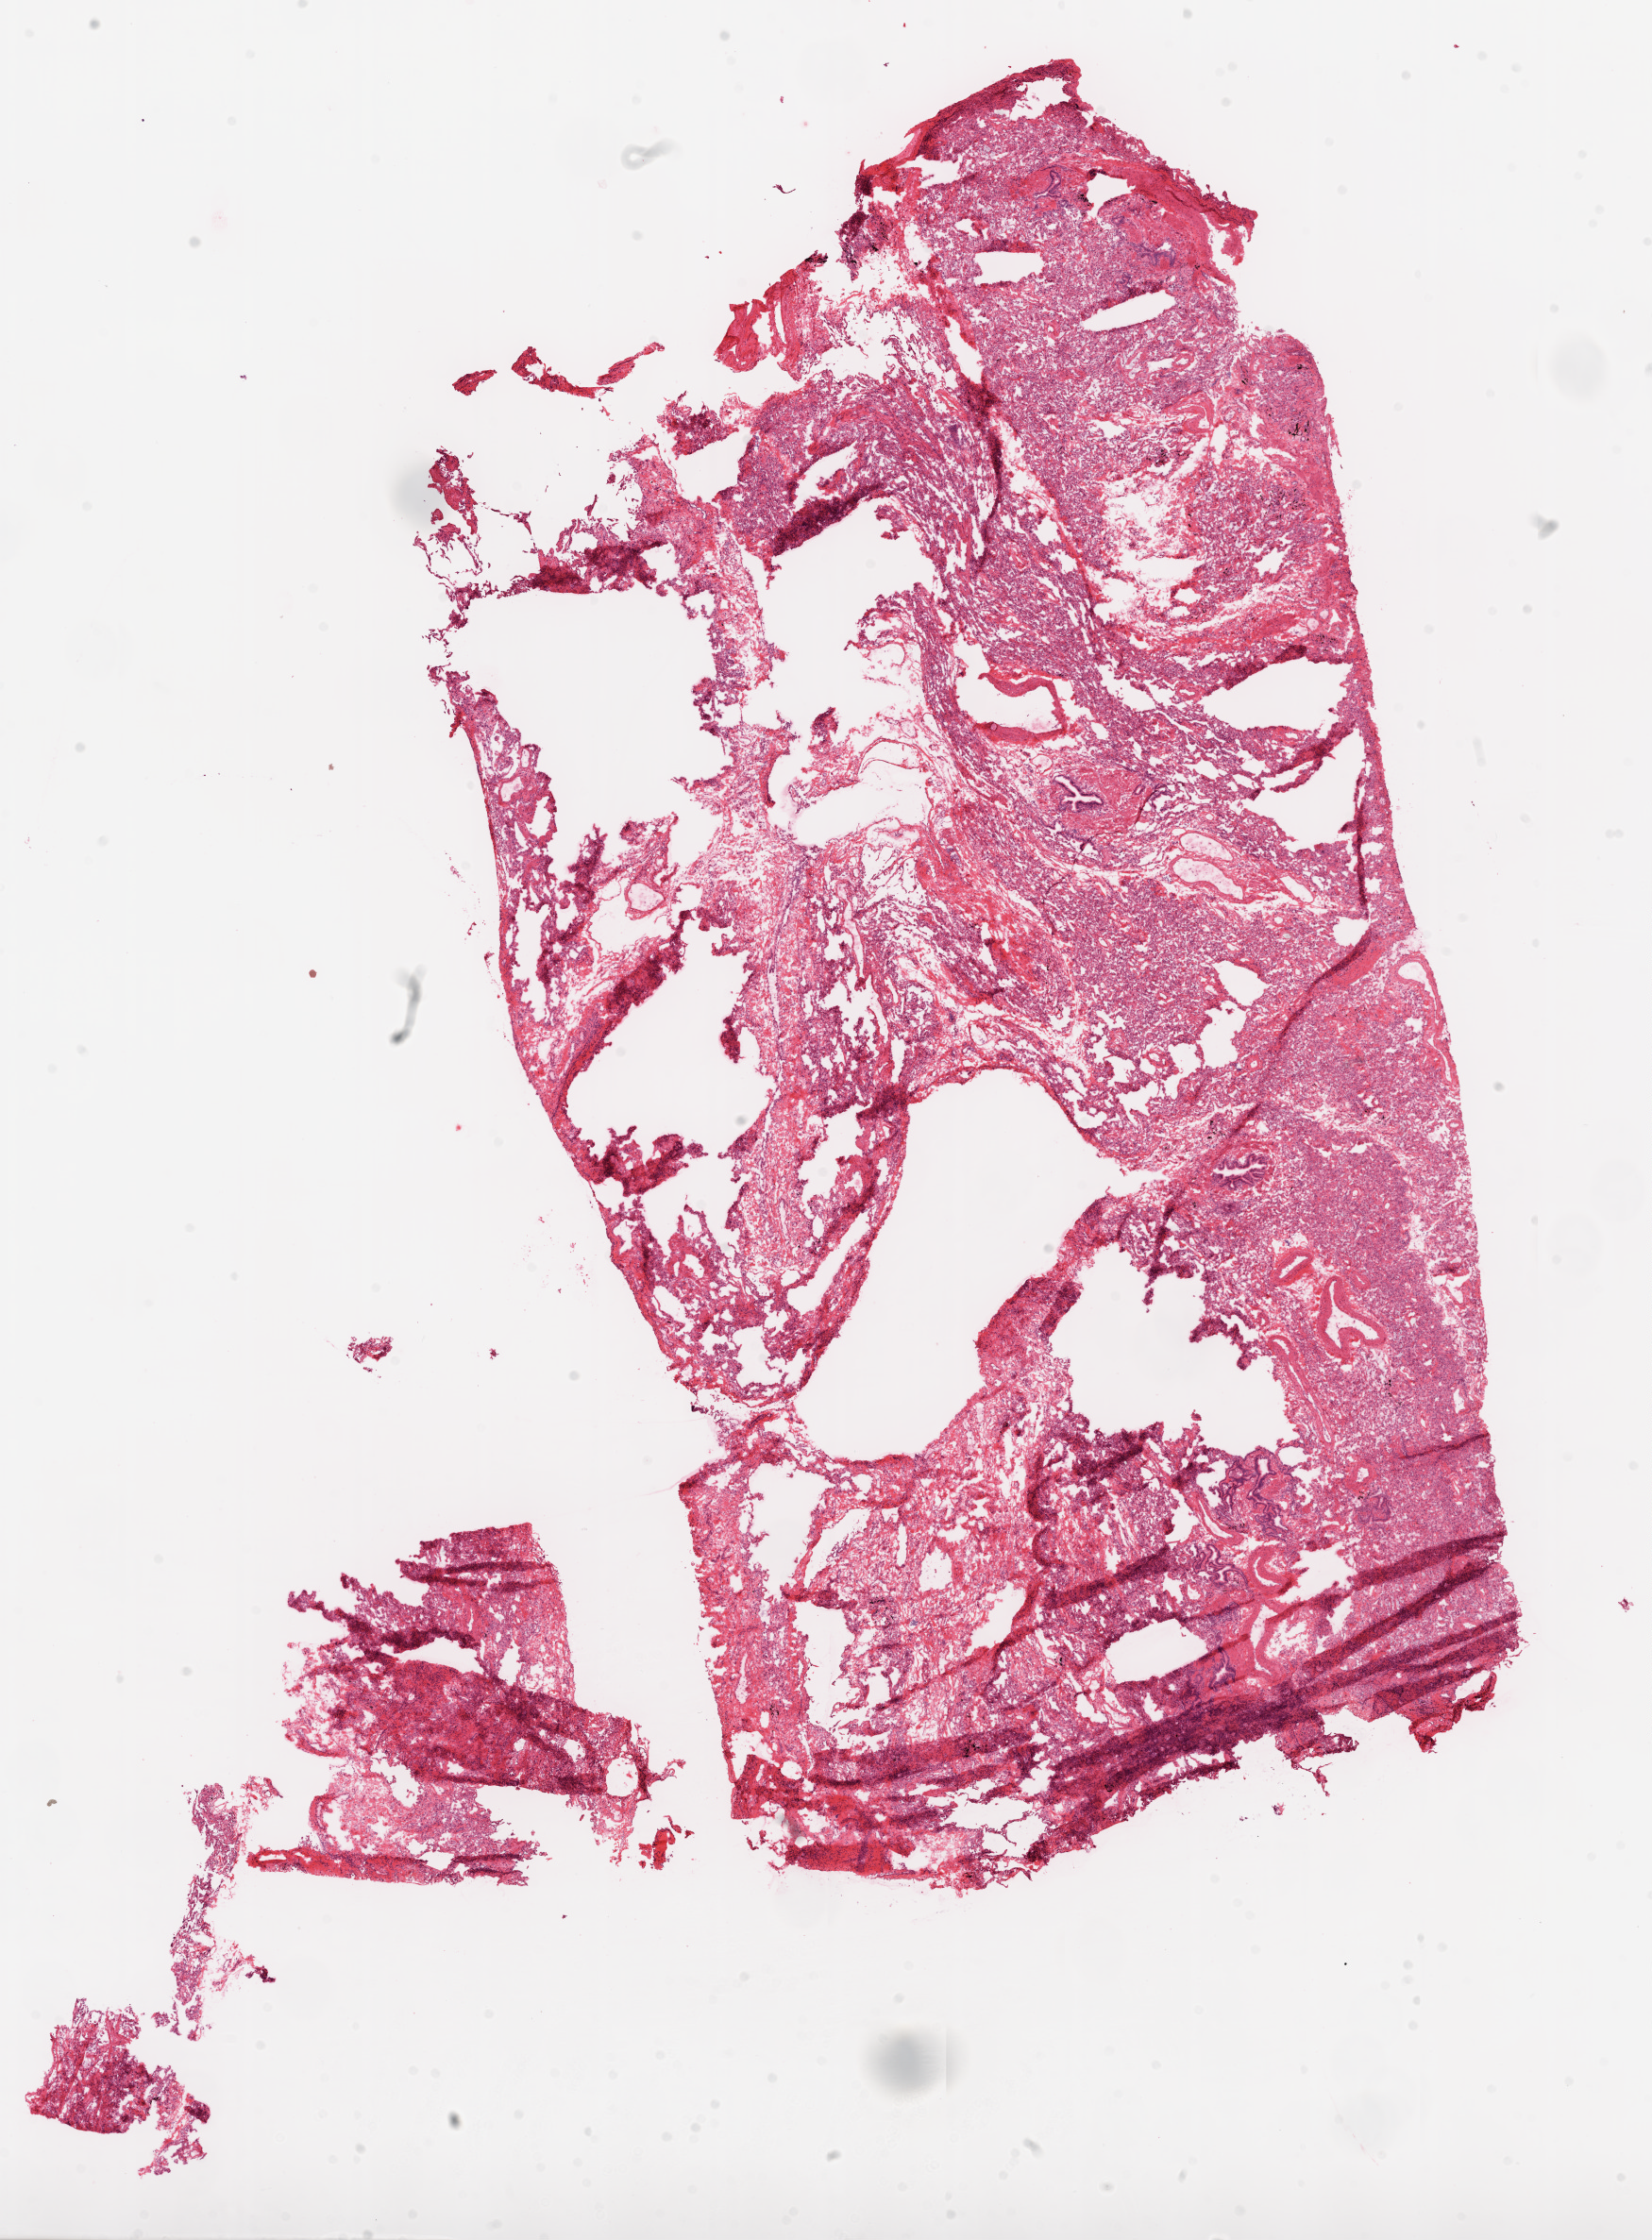
Hematoxylin and eosin (H&E) stained whole-slide image — whole scanned area (about 14.0 x 19.0 mm, from a 20x scan) shown as a low-resolution overview. Frozen section. Solid tissue normal (non-tumour tissue) sample from the lung. Patient: male, age at initial diagnosis 73 years.
• this section: solid tissue normal sample (biorepository sample class)
• patient diagnosis: Squamous cell carcinoma, NOS